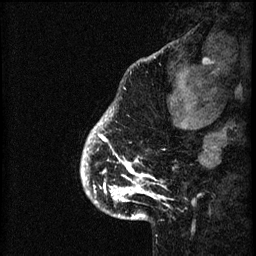
Breast MRI (dynamic contrast-enhanced), one sagittal slice; position 10 of 60 along the scan axis; 3 images stored at this slice position (order not interpretable as contrast timing); 1.5 T; TE 4.2 ms, TR 8.2 ms; 256 × 256 image matrix, field of view 180 × 180 mm. Female patient, age 41 years.
Annotated regions visible in this slice (semi-automatic segmentation, software-assisted and operator-edited):
- analysis volume of interest (the breast-tissue region the enhancement analysis was run in; not a lesion): bounding box (x1, y1, x2, y2) in pixels: (82, 108, 176, 205)
- tumour enhancement mask (voxels above the 70 % enhancement threshold inside the analysis volume of interest): (82, 118, 166, 203)